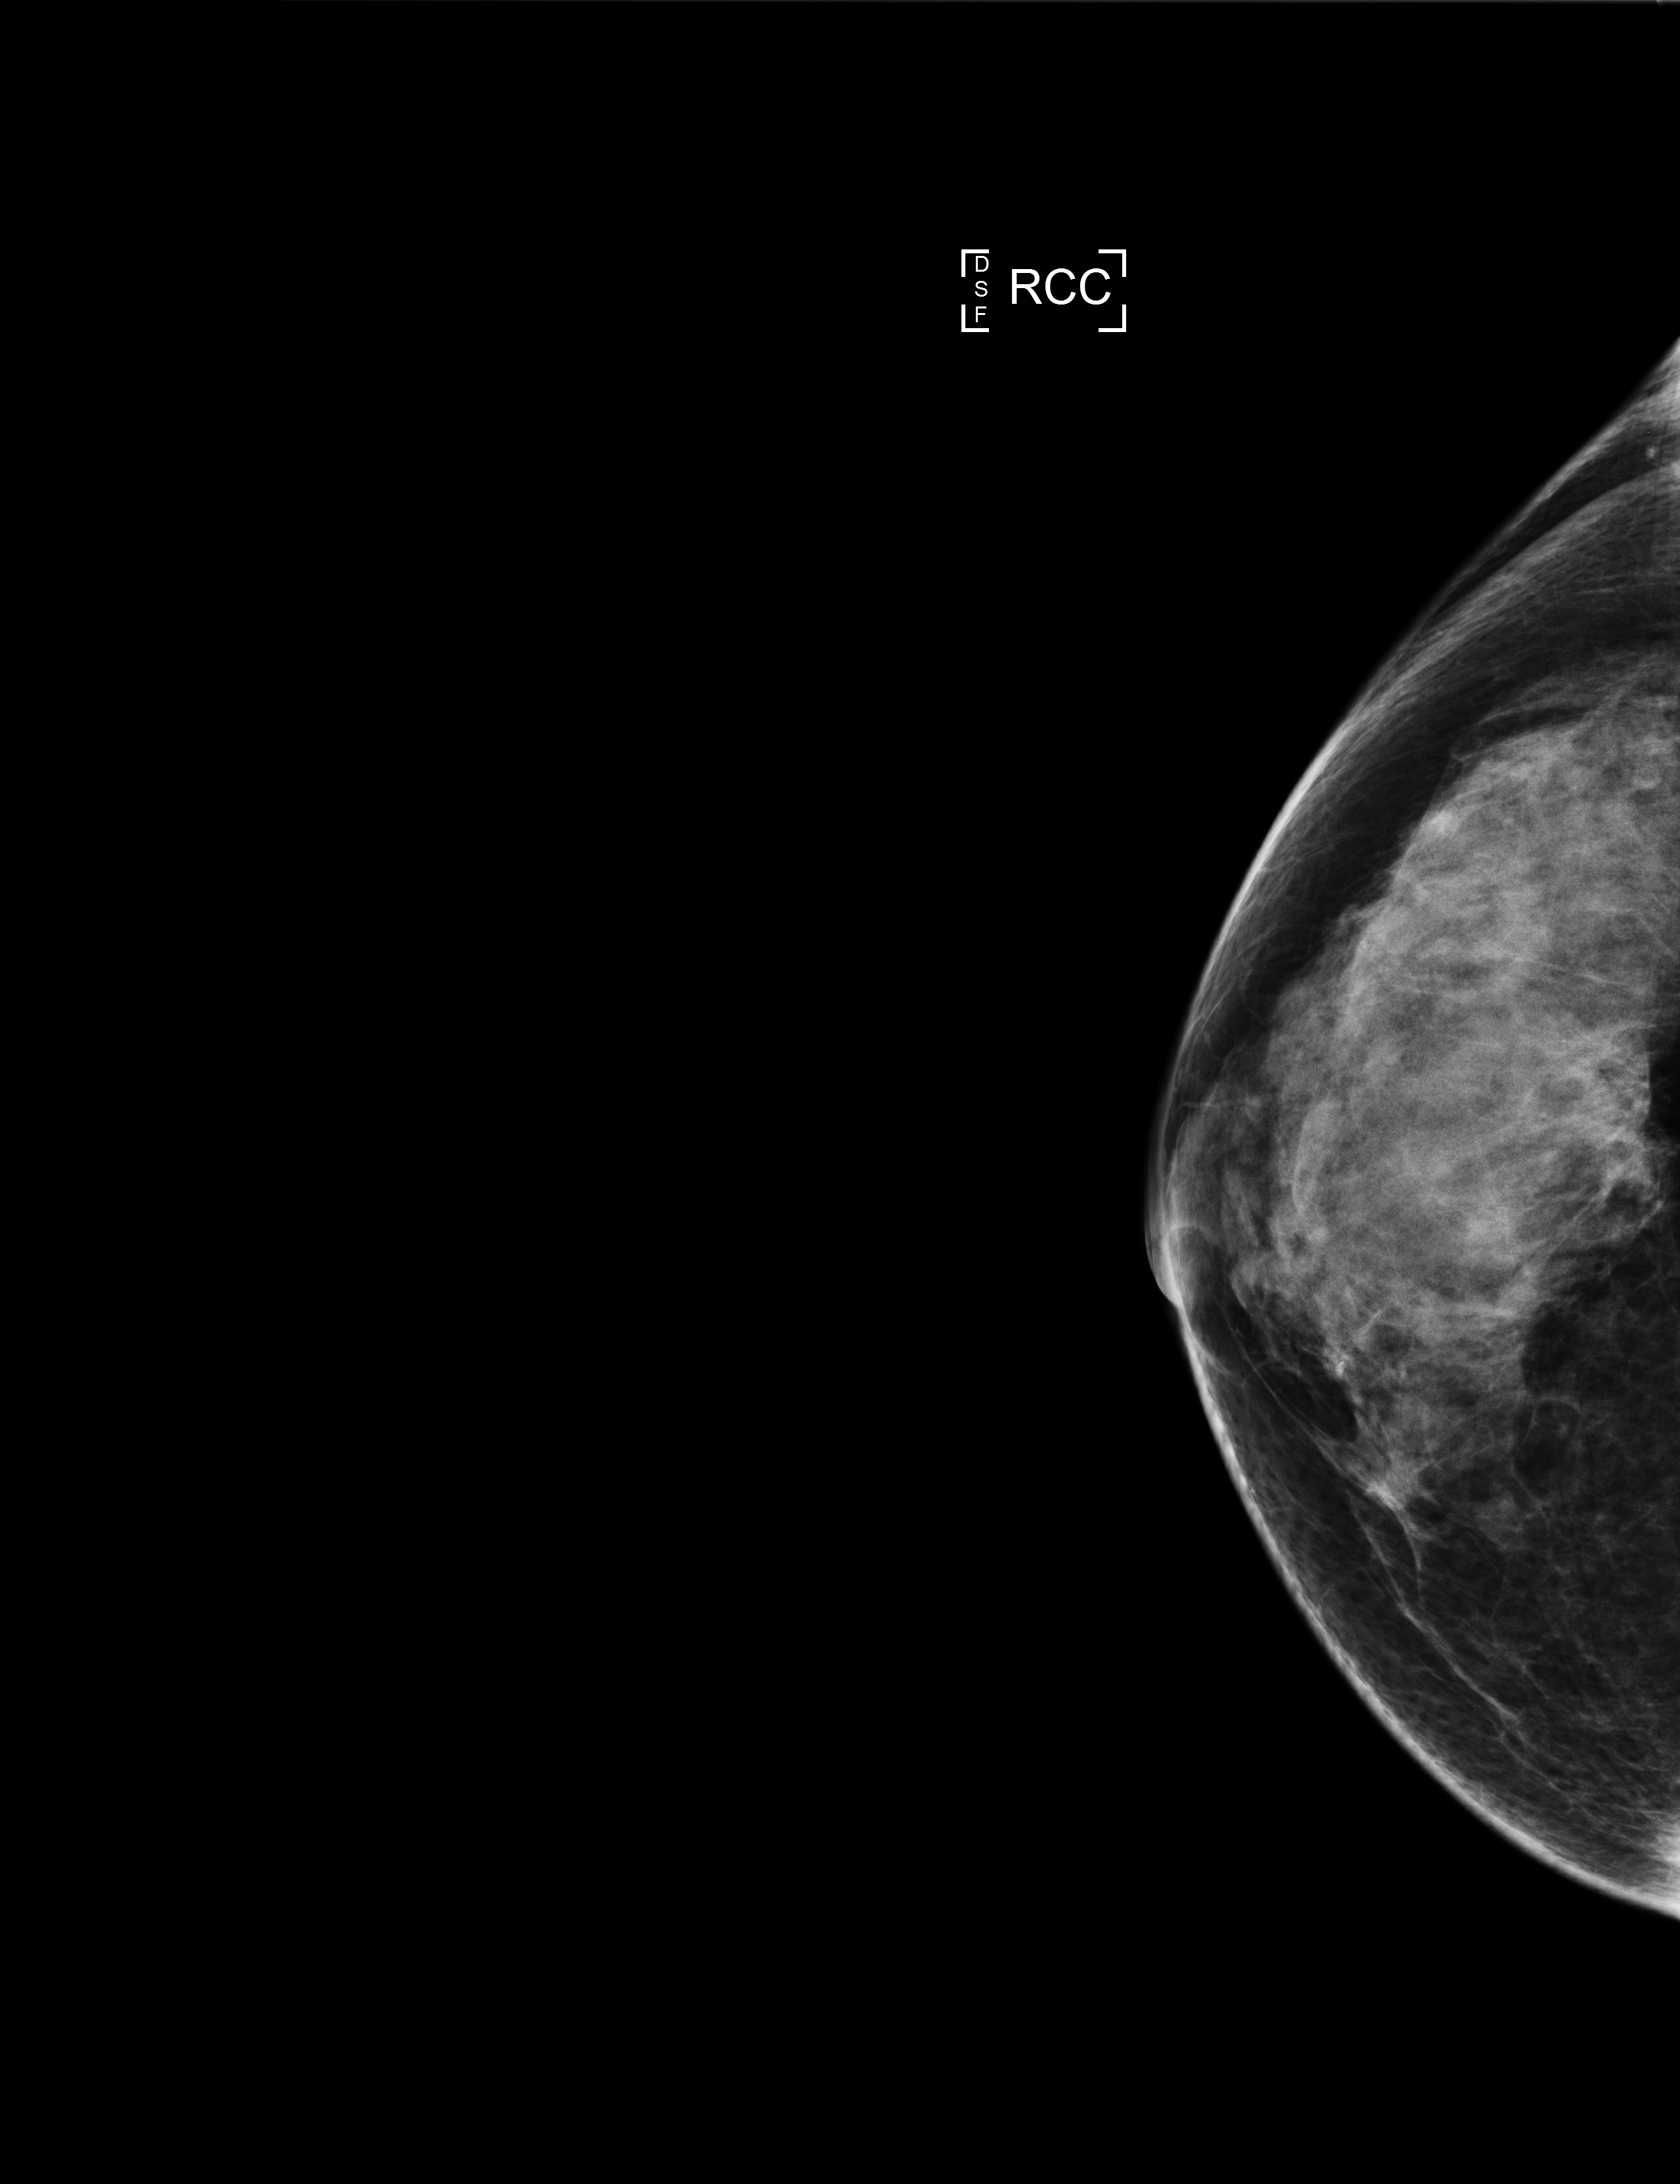
Digital mammogram (FFDM); right breast; CC view; screening examination; compressed breast thickness 58 mm. Female patient, age 50 years.
- BI-RADS breast density category at the screening exam (both breasts, scale 1–4): 4
- final BI-RADS assessment for this screening round (tomosynthesis exam, both breasts): category 1
- recall: no recall after this screen